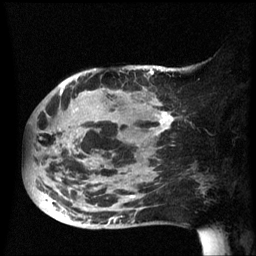
Breast MRI (dynamic contrast-enhanced), one sagittal slice; dynamic contrast-enhanced series, image 2 of 3 at this slice position (ordered by acquisition); 1.5 T; TE 4.2 ms, TR 8.4 ms; 2.5 mm slice thickness; 256 × 256 image matrix. Female patient, age 49 years.
Annotated regions visible in this slice (semi-automatically segmented with operator editing):
- analysis volume of interest (the breast-tissue region the enhancement analysis was run in; not a lesion): box from (x=25, y=72) to (x=175, y=229) px
- tumour enhancement mask (voxels above the 70 % enhancement threshold inside the analysis volume of interest): (x=56, y=72)–(x=175, y=225)